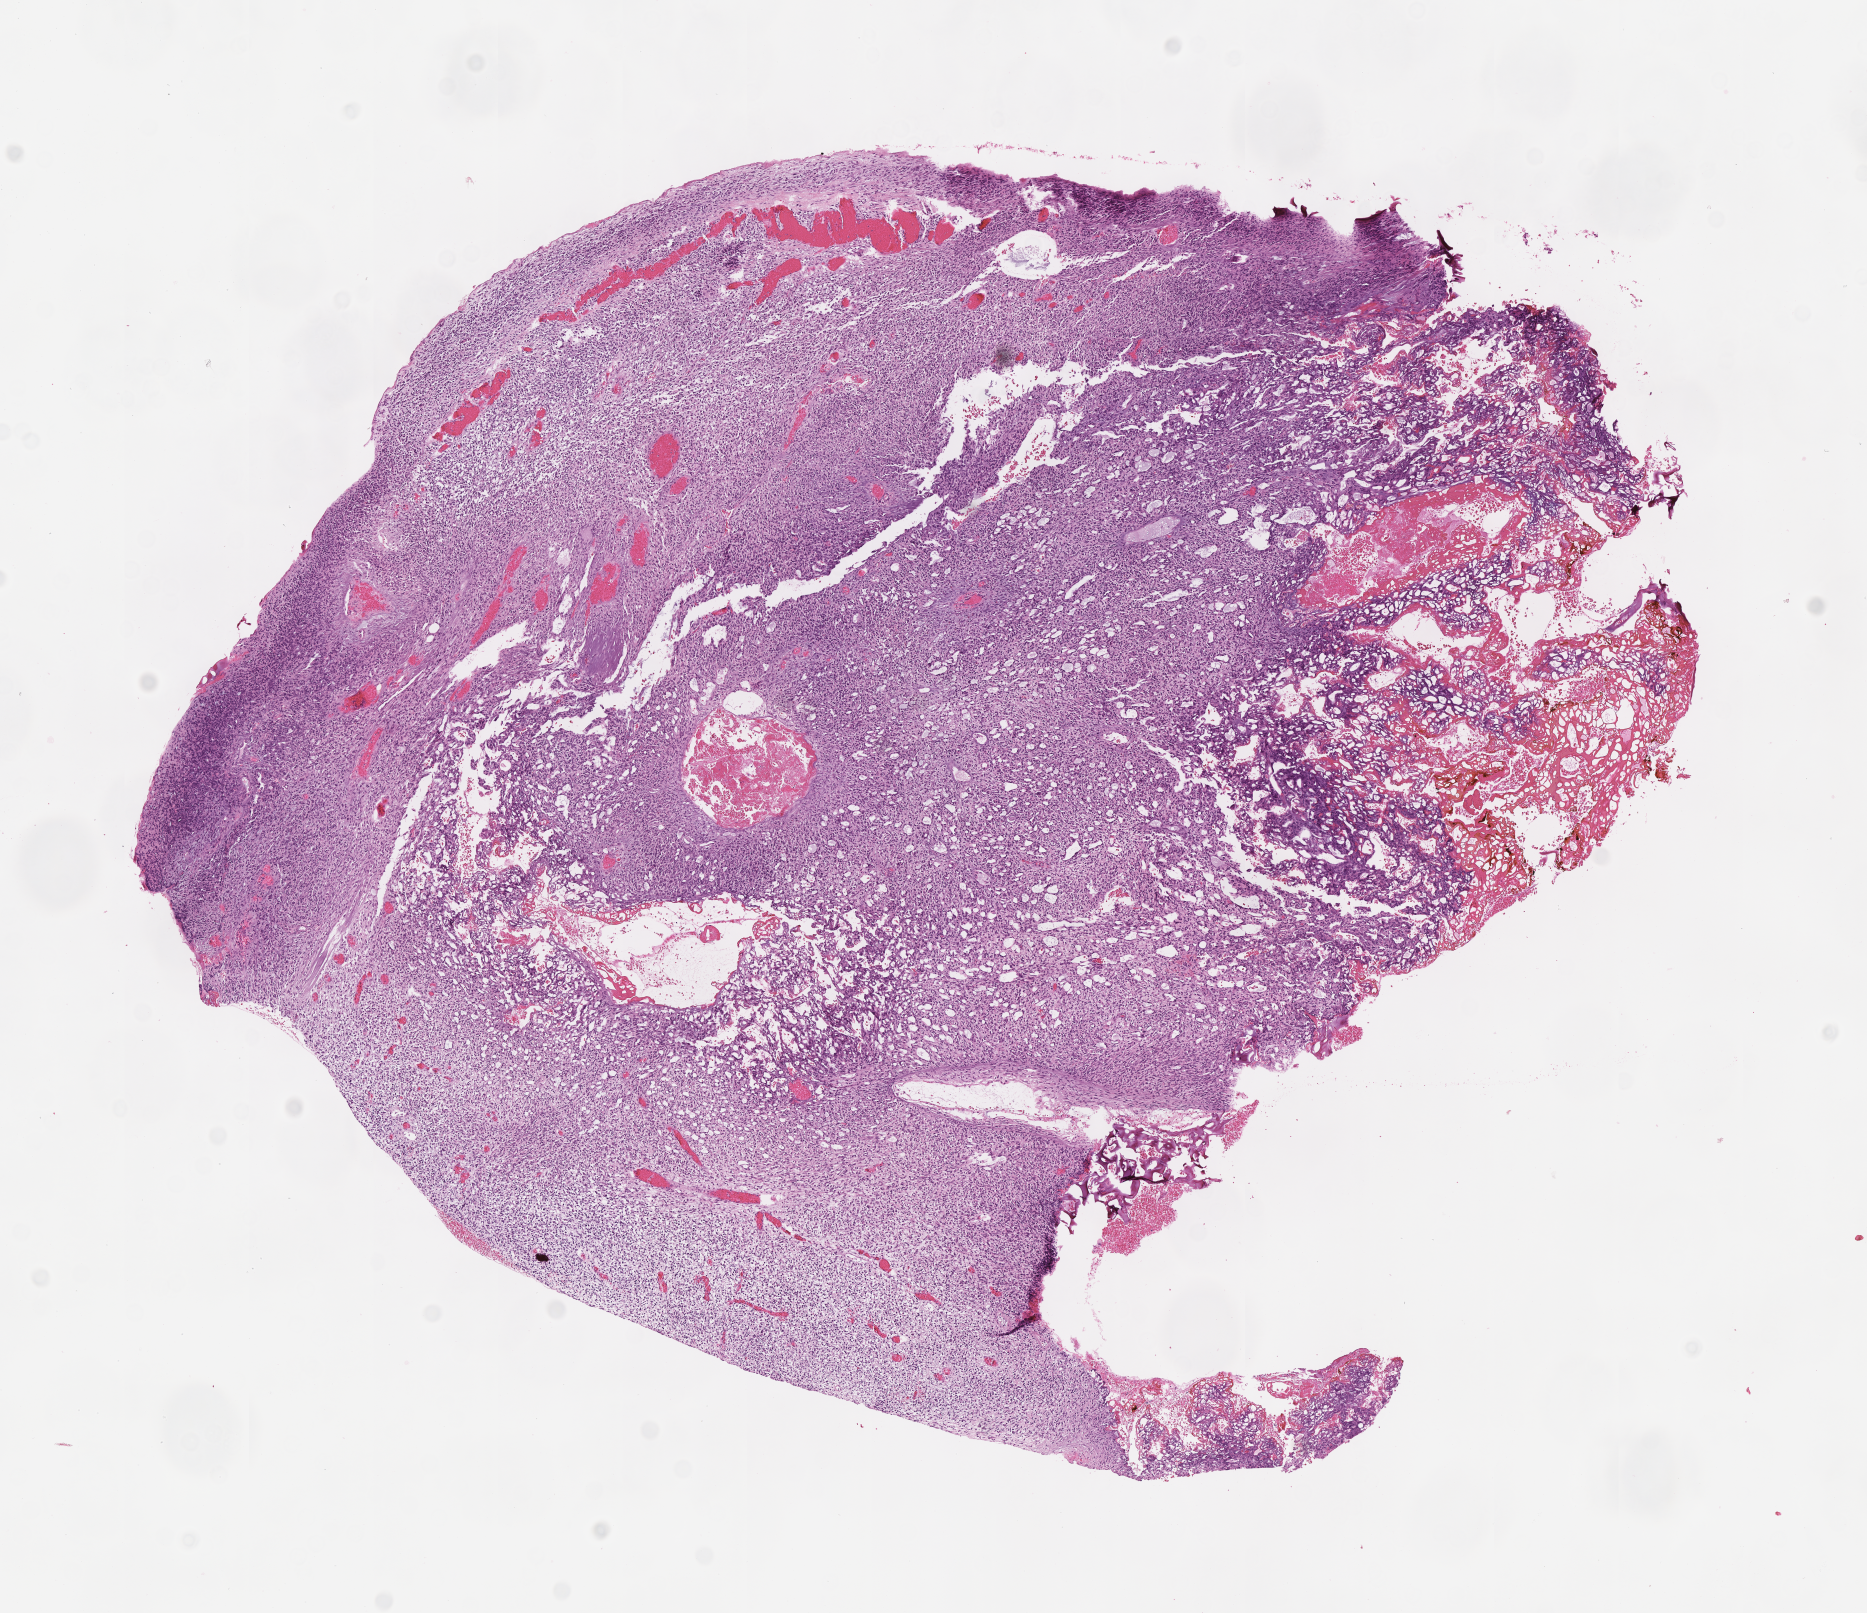
Digitized H&E-stained section of tumor tissue — low-resolution overview of the scanned area, about 7.5 x 6.5 mm, formalin-fixed, paraffin-embedded (FFPE) tissue, site: abdomen. Male patient, age at diagnosis 0.2 years.
Metastatic status at presentation (as recorded): non-metastatic (unconfirmed). Stage (as recorded): 3. Diagnosis: rhabdomyosarcoma; histological classification: embryonal rhabdomyosarcoma.